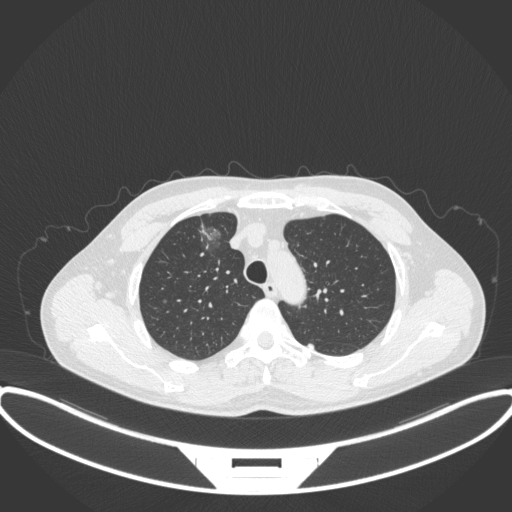
Chest CT, one axial slice; slice 283 of 395 in the series (ordered by position); 120 kVp; lung window (W 1500 / L -600 HU); 512 × 512 image matrix, field of view 424 × 424 mm. Male patient, age 60 years. From the clinical record (not read from this slice): clinical TNM (as recorded): T1c N0 M0.
Structures marked on this image (bounding box drawn by a radiologist):
- lung tumour (recorded histology: adenocarcinoma): bounding box [x1, y1, x2, y2] px = [196, 218, 226, 263]